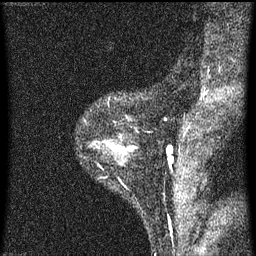
Breast MRI (dynamic contrast-enhanced), one sagittal slice; position 16 of 60 along the scan axis; dynamic contrast-enhanced series, image 2 of 3 at this slice position (ordered by acquisition); 1.5 T; TE 4.2 ms, TR 8 ms; 2 mm slice thickness; 256 × 256 image matrix, field of view 180 × 180 mm. Female patient, age 33 years.
Annotated regions visible in this slice (semi-automatic segmentation, software-assisted and operator-edited):
- analysis volume of interest (the breast-tissue region the enhancement analysis was run in; not a lesion): bounding box <95,140,136,165> (left, top, right, bottom; pixels)
- tumour enhancement mask (voxels above the 70 % enhancement threshold inside the analysis volume of interest): <109,144,131,151>